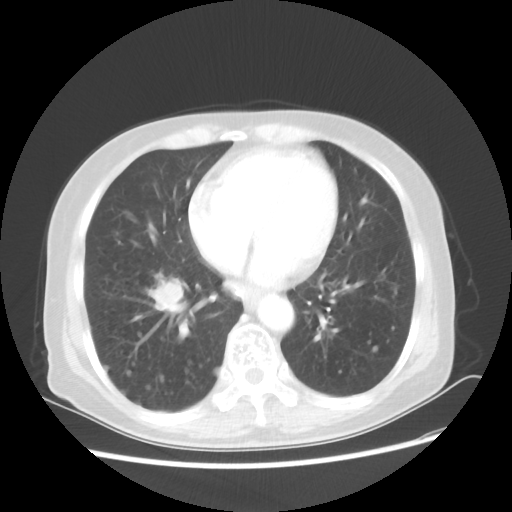
Chest CT, one axial slice; slice 21 of 56 in the series (ordered by position); reconstruction kernel STANDARD; 80 kVp; lung window (W 1500 / L -600 HU); 5 mm slice thickness; 512 × 512 image matrix. Female patient, age 68 years. From the clinical record (not read from this slice): clinical TNM (as recorded): T1c N3 M0.
Outlined on this slice (rectangle marked by the reading radiologist):
- lung tumour (recorded histology: squamous cell carcinoma): bounding box (x1, y1, x2, y2) in pixels: (139, 273, 202, 320)